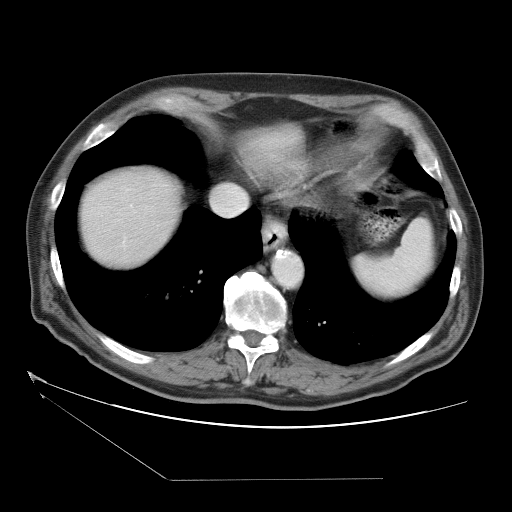
Contrast-enhanced abdominal CT (liver protocol), one axial slice; slice 32 of 38 in the series (ordered by position); reconstruction kernel STANDARD; one of 2 acquisitions stored at this slice position; soft-tissue window (W 400 / L 40 HU); 5 mm slice thickness; 512 × 512 image matrix, field of view 400 × 400 mm. Case-level facts recorded for this patient, not image findings: diagnosis: hepatocellular carcinoma (patient treated with transarterial chemoembolisation; whether this scan precedes or follows treatment is not stated here); TNM stage (as recorded): Stage-II; Child-Pugh class: A.
Outlined on this slice (semi-automatic segmentation, software-assisted and operator-edited):
- liver parenchyma outside the tumour (the mass and vessels are separate outlines, so this box may not span the whole liver): bounding box (x1, y1, x2, y2) in pixels: (80, 132, 294, 266)
- liver vessels: (122, 236, 127, 248)